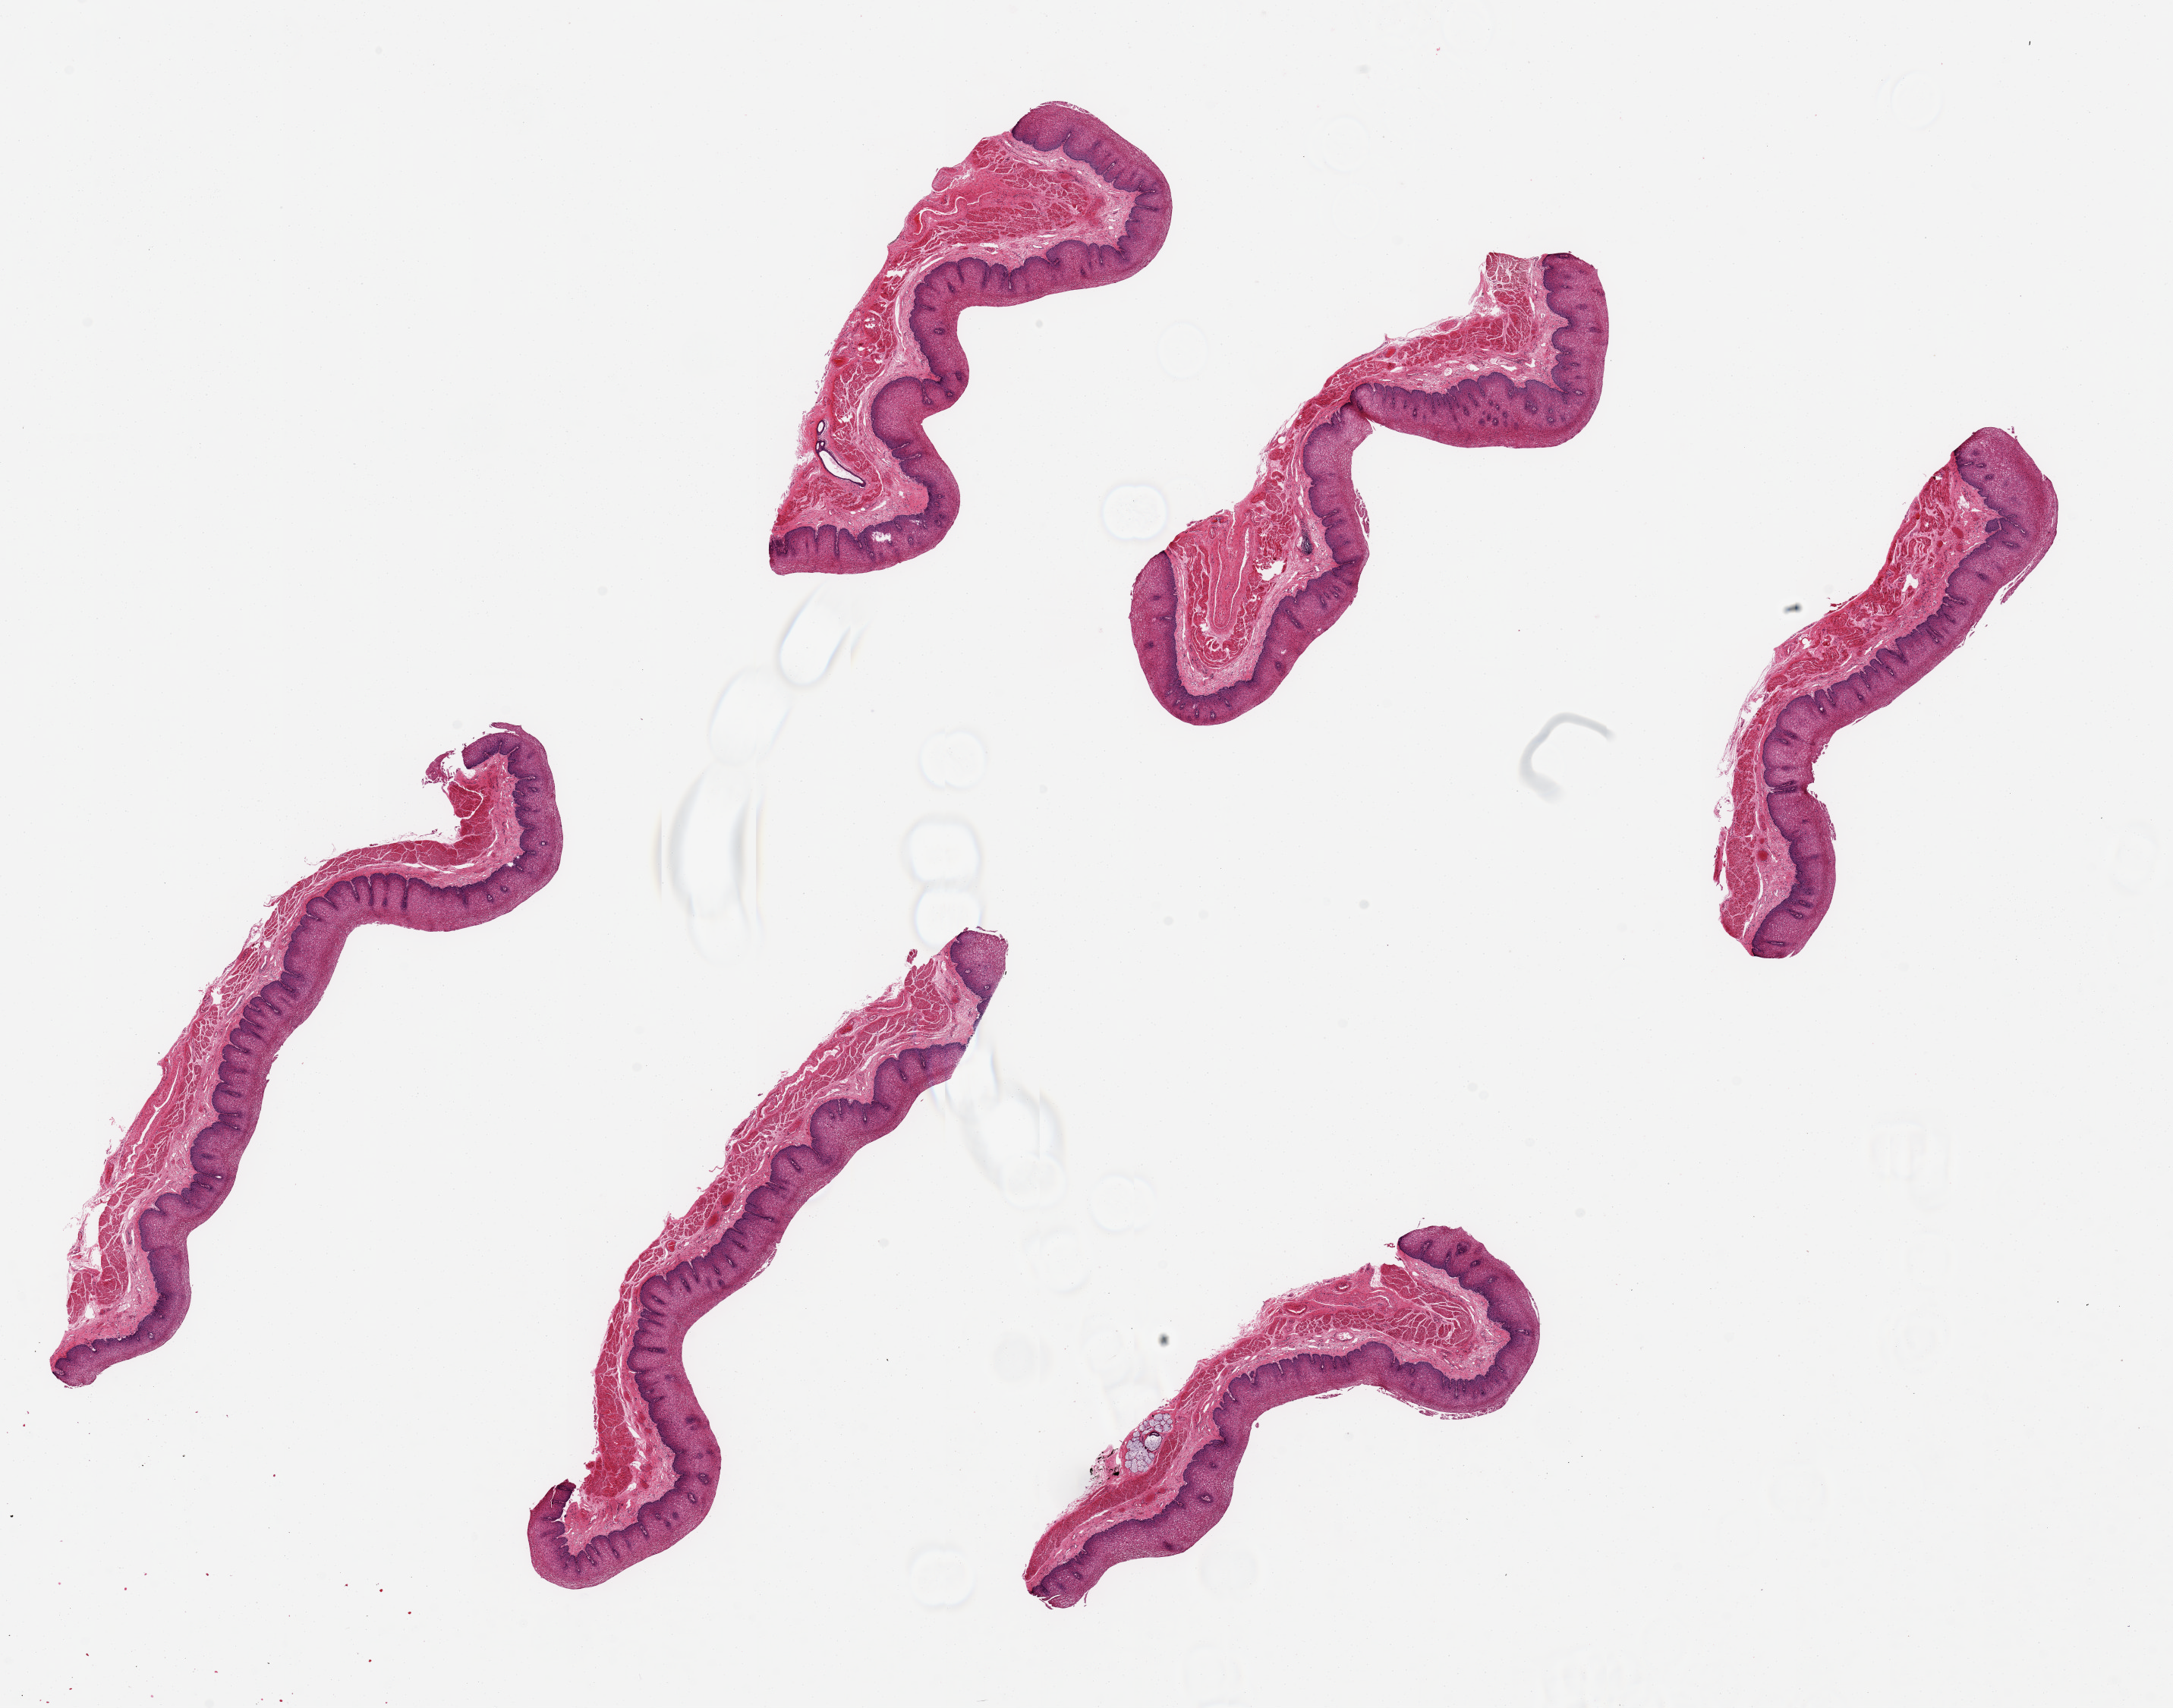
H&E whole-slide image, brightfield, low-resolution overview of the scanned area, about 22.6 x 17.8 mm; PAXgene-fixed paraffin-embedded (PFPE) section; sampled site (target tissue): esophageal mucous membrane; tissue donor sample. Donor: male.
- review note (as recorded): 6 pieces ~7x1mm. Squamous mucosa, well preserved, is ~40-50% of thickness